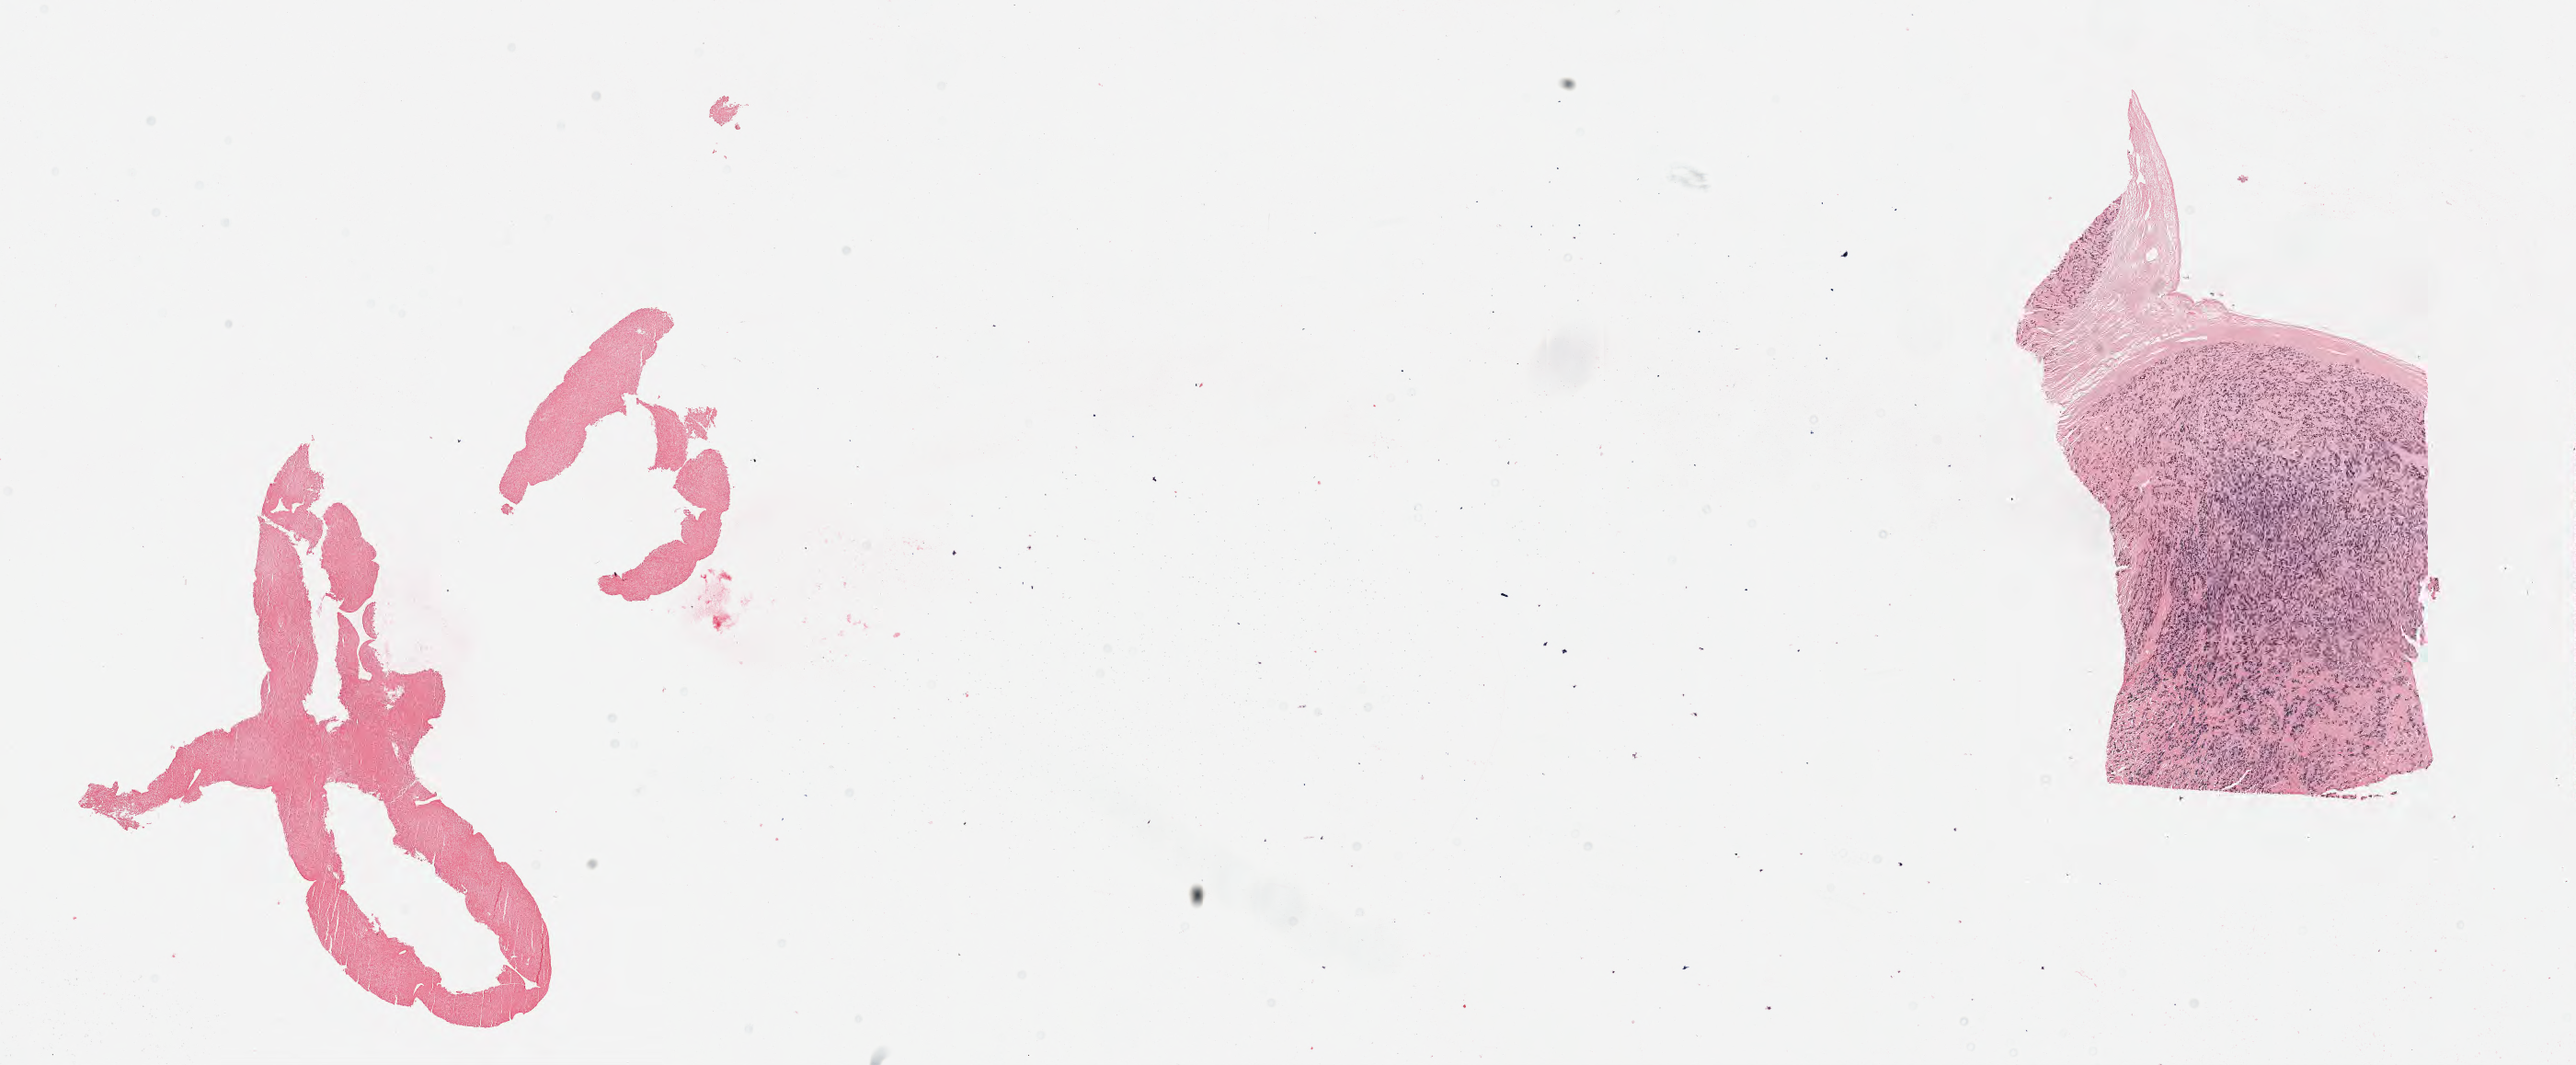
In-situ hybridisation whole-slide image, Epstein–Barr virus-encoded RNA (EBER) probe, shown as a low-resolution overview of the whole scanned area (about 22.6 x 9.4 mm). Male patient, aged 52.
Specimen: tumor tissue; site: liver.